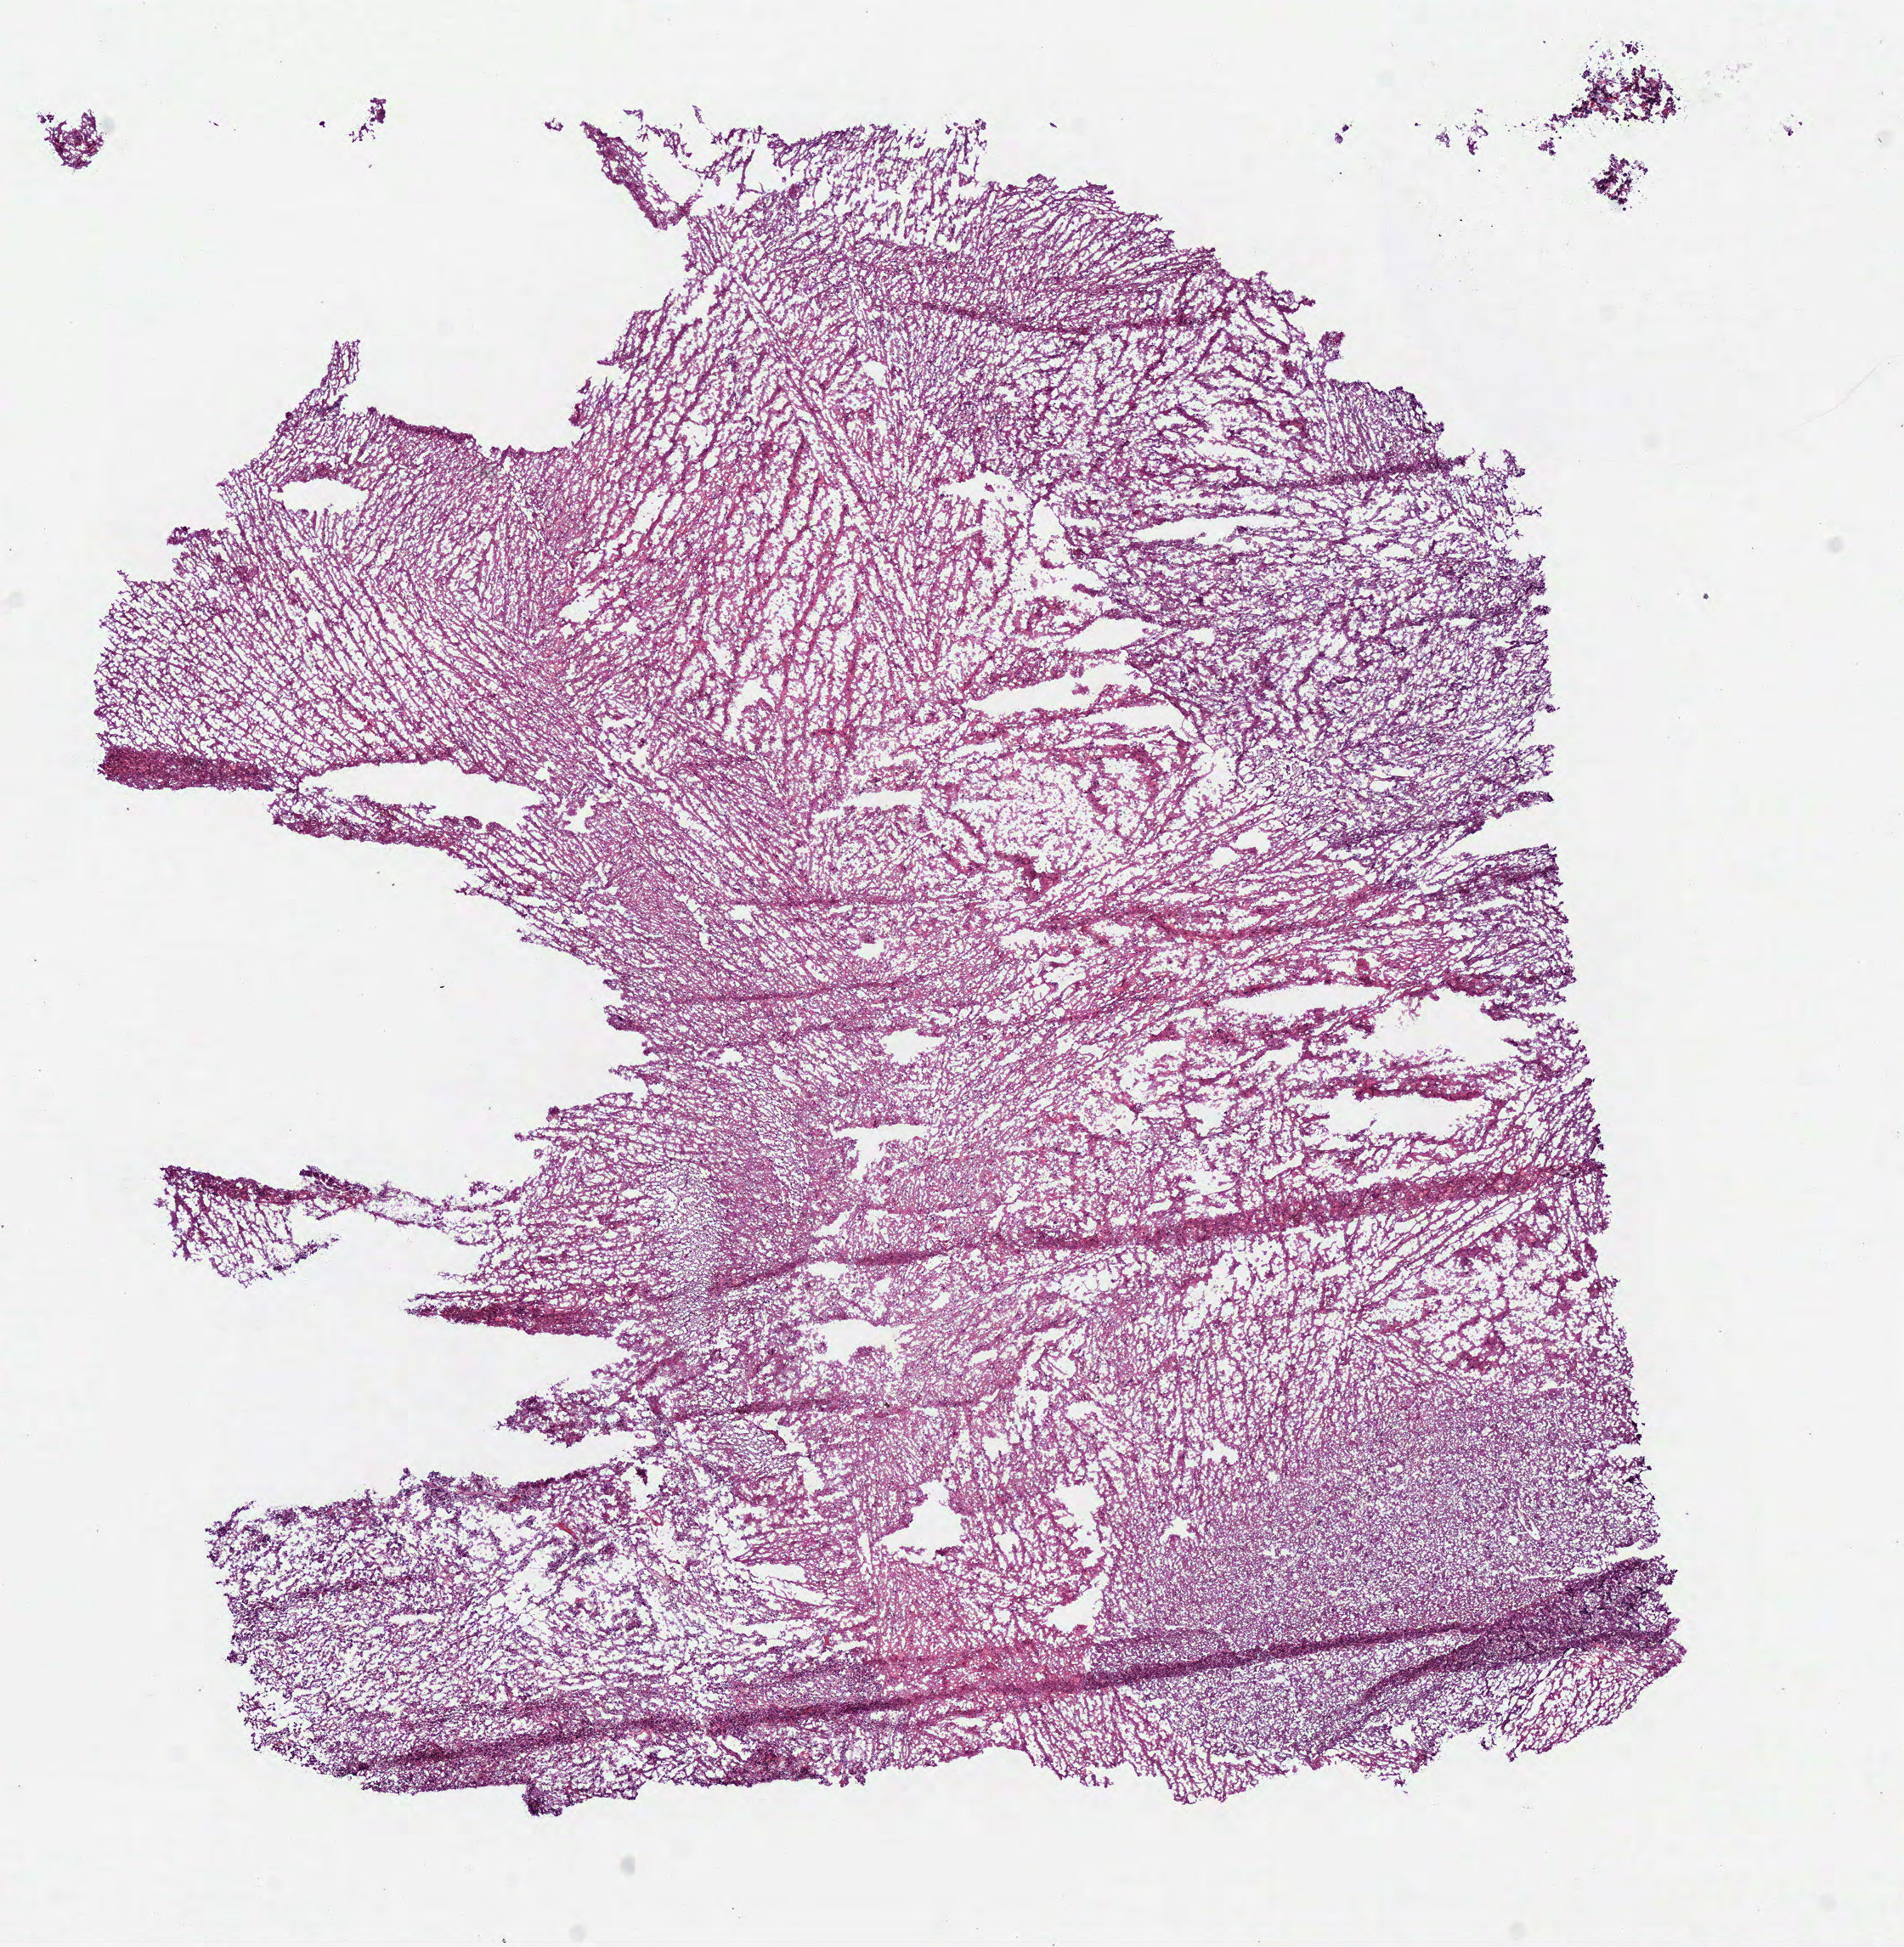
Digitized Hematoxylin and eosin (H&E) stained tissue section (whole slide), a low-resolution overview of the entire scanned area, about 8.8 x 9.0 mm (acquisition: 40x scan), frozen section from the bottom of the tissue portion, sample: primary tumour, brain. Male patient; age at initial diagnosis 78 years. Composition of this section per pathologist review: tumour cells 95%, tumour nuclei 70%, normal cells 0%, stromal cells 0%, necrosis 5%.
- diagnosis: Glioblastoma